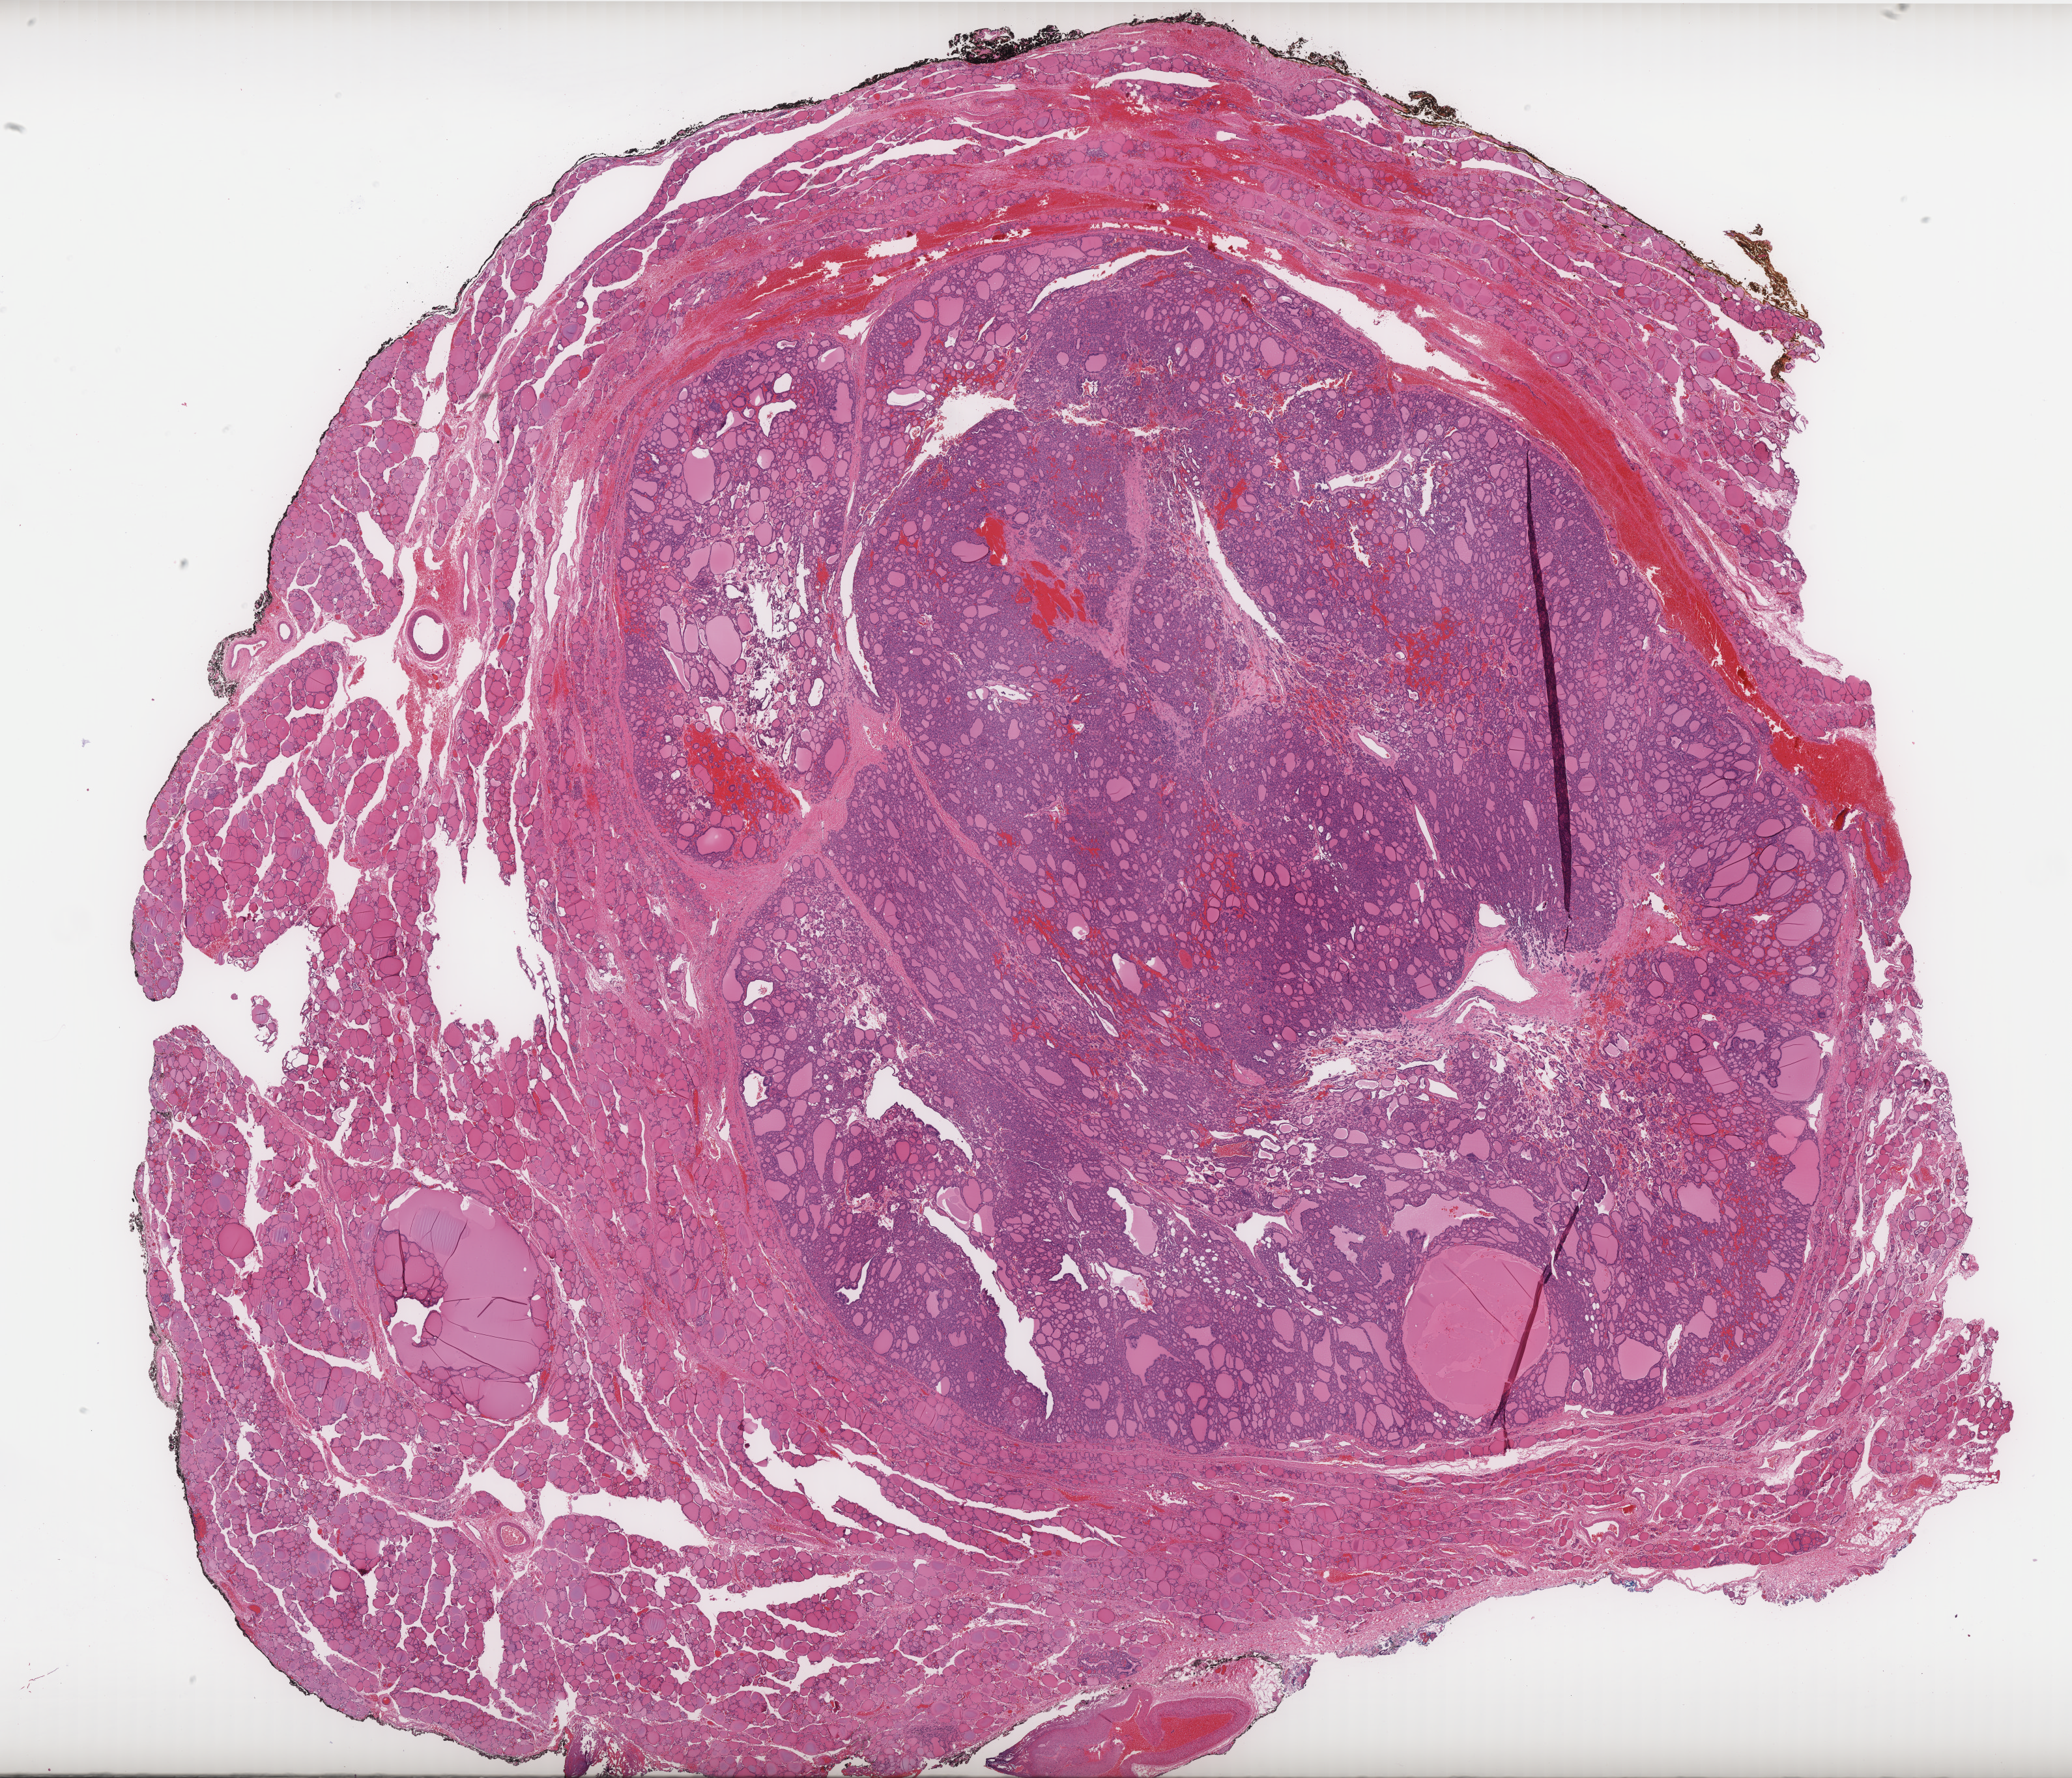
Whole-slide histology image, H&E-stained, shown as a low-resolution overview of the whole scanned area (about 25.5 x 21.9 mm); FFPE section; primary tumour sample from the thyroid. Patient: male, age at initial diagnosis 55 years.
AJCC pathologic stage: II. Pathologic diagnosis: Papillary adenocarcinoma, NOS (thyroid gland). Laterality: bilateral.